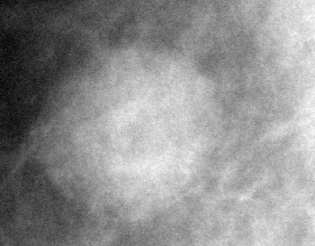
Cropped region of a digitized screen-film mammogram centred on a radiologist-marked abnormality; right breast; MLO view; BI-RADS breast density category 3 (scale 1–4).
Finding: mass, shape round, margins circumscribed; BI-RADS assessment category 5; subtlety rating 5 on a 1 (subtle) to 5 (obvious) scale; pathology (as recorded): malignant.